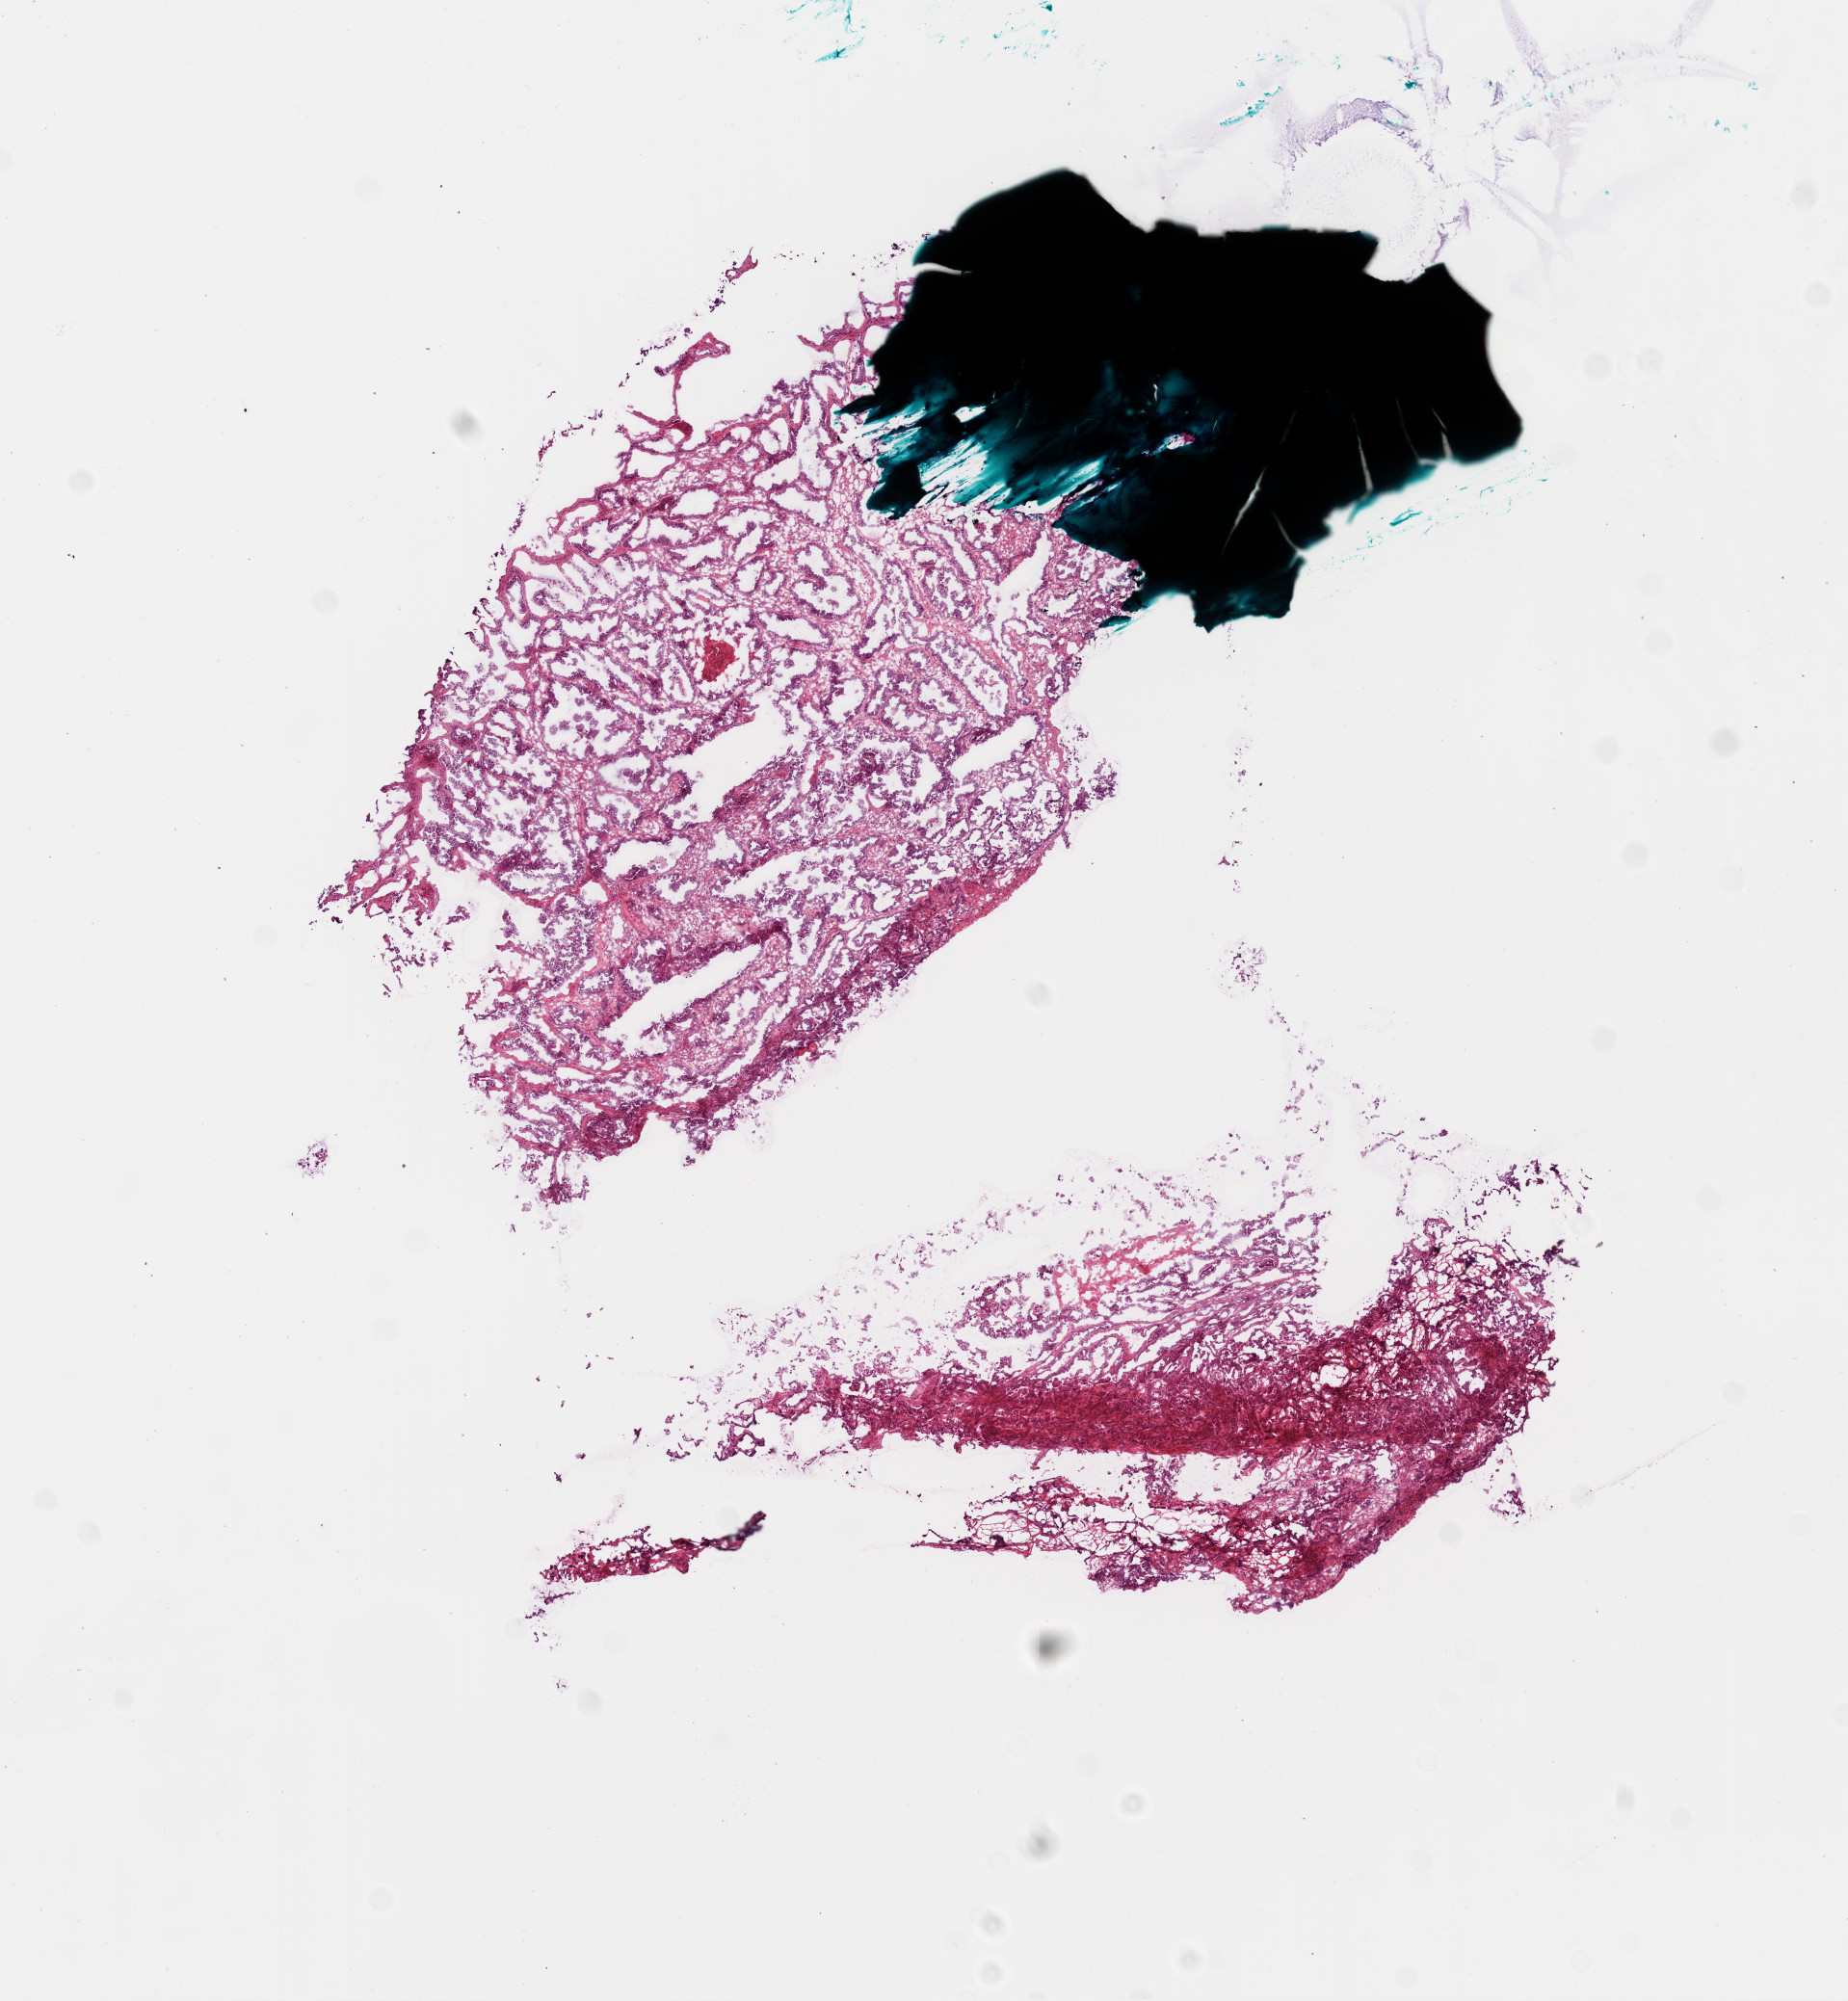
H&E-stained whole-slide image, a low-resolution overview of the entire scanned area, about 7.7 x 8.4 mm (from a 20x scan). Frozen section from the bottom of the tissue portion. Ovary, primary tumour sample. Patient: female, age at initial diagnosis 52 years. Histologic grade: G3 (poorly differentiated). Slide review estimates, as recorded: tumour cells 85%, tumour nuclei 80%, normal cells 10%, stromal cells 5%, necrosis 0%.
FIGO stage: IV. Diagnosis: Serous cystadenocarcinoma, NOS. Laterality: right.